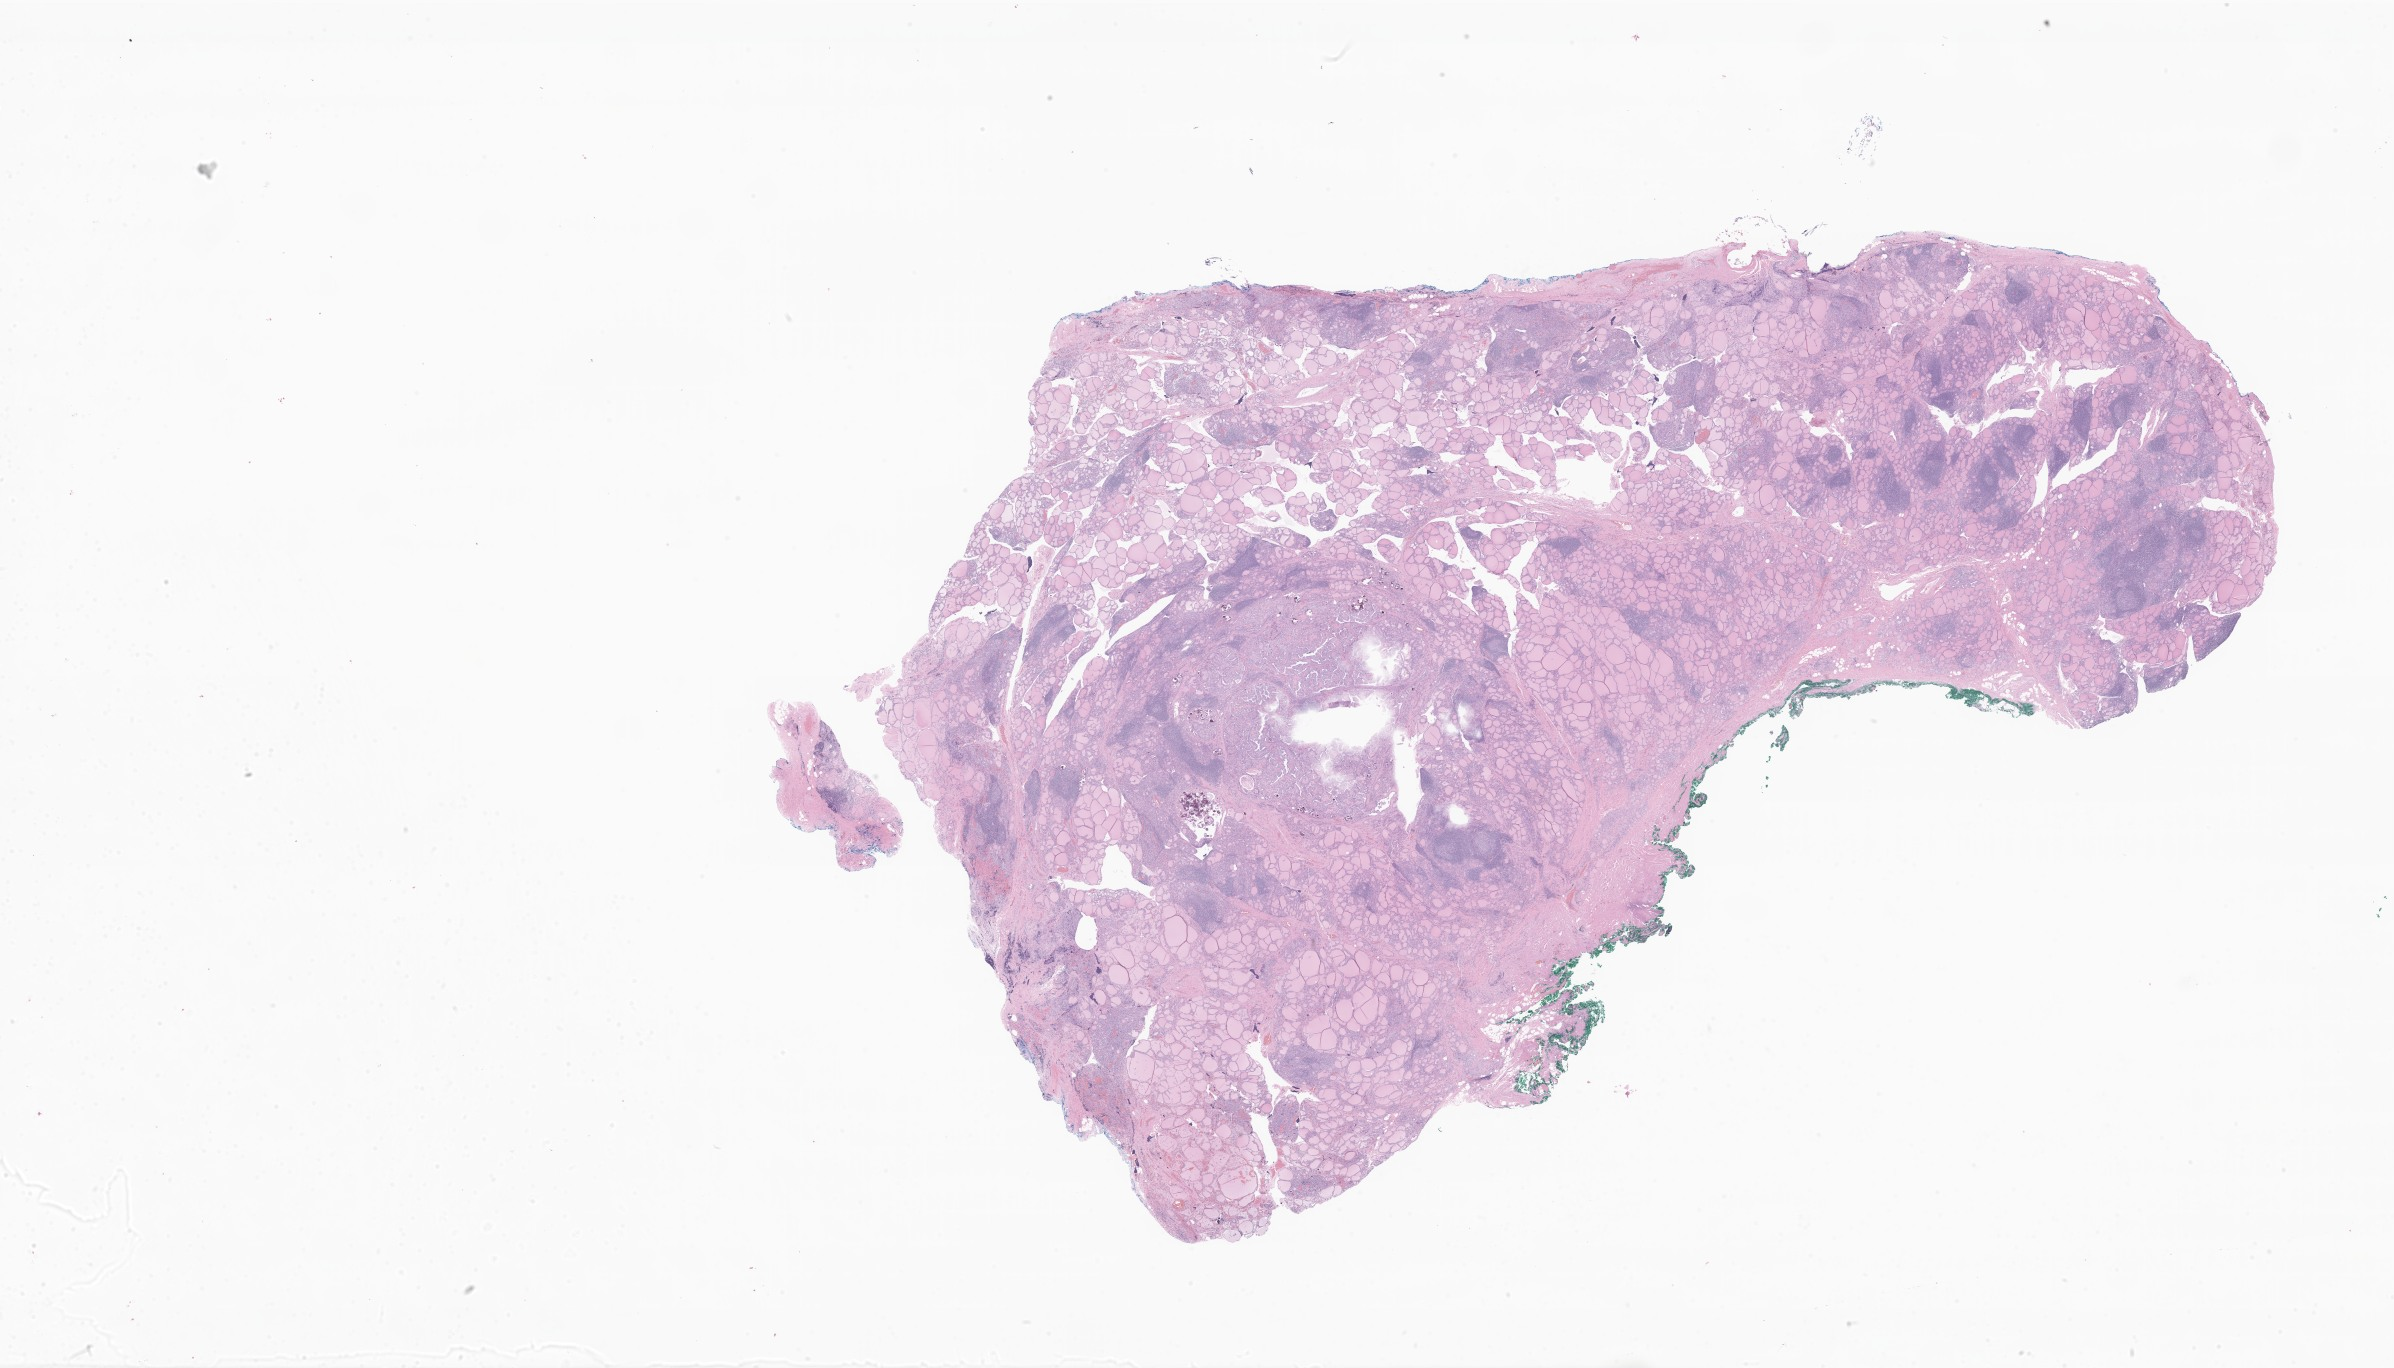
Digitized haematoxylin and eosin-stained section of tumor tissue from the thyroid, a low-resolution overview of the entire scanned area, about 40.4 x 23.1 mm. Formalin-fixed paraffin-embedded section. Patient female; age 192 months (16 years).
* diagnosis: Papillary carcinoma, NOS